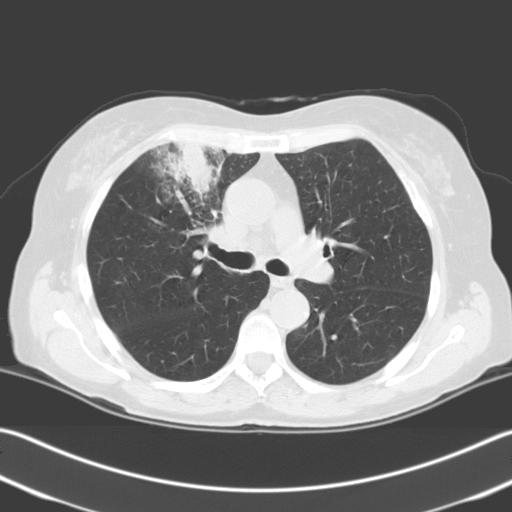
Low-dose screening chest CT, one axial slice. Position 137 of 204 along the scan axis. Lung window (W 1500 / L -600 HU). 3.2 mm slice thickness. 512 × 512 image matrix, field of view 348 × 348 mm.
Outlined on this slice (expert manual segmentation):
- lesion 1 (tumor, upper lobe of right lung): bounding box (x1, y1, x2, y2) in pixels: (175, 143, 217, 195)